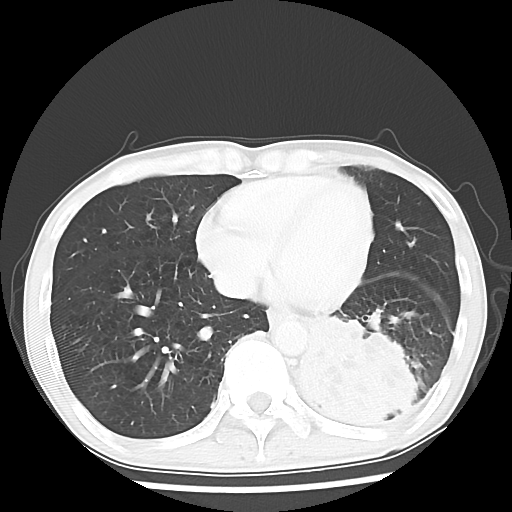
Chest CT, one axial slice; slice 20 of 64 in the series (ordered by position); reconstruction kernel LUNG; 120 kVp; lung window (W 1500 / L -600 HU); 512 × 512 image matrix, field of view 313 × 313 mm. Patient: male, 68 years. Case-level facts recorded for this patient, not image findings: clinical TNM (as recorded): T4 N0 M0.
Annotated regions visible in this slice (rectangle marked by the reading radiologist):
- lung tumour (recorded histology: squamous cell carcinoma): bounding box <291,314,445,439> (left, top, right, bottom; pixels)